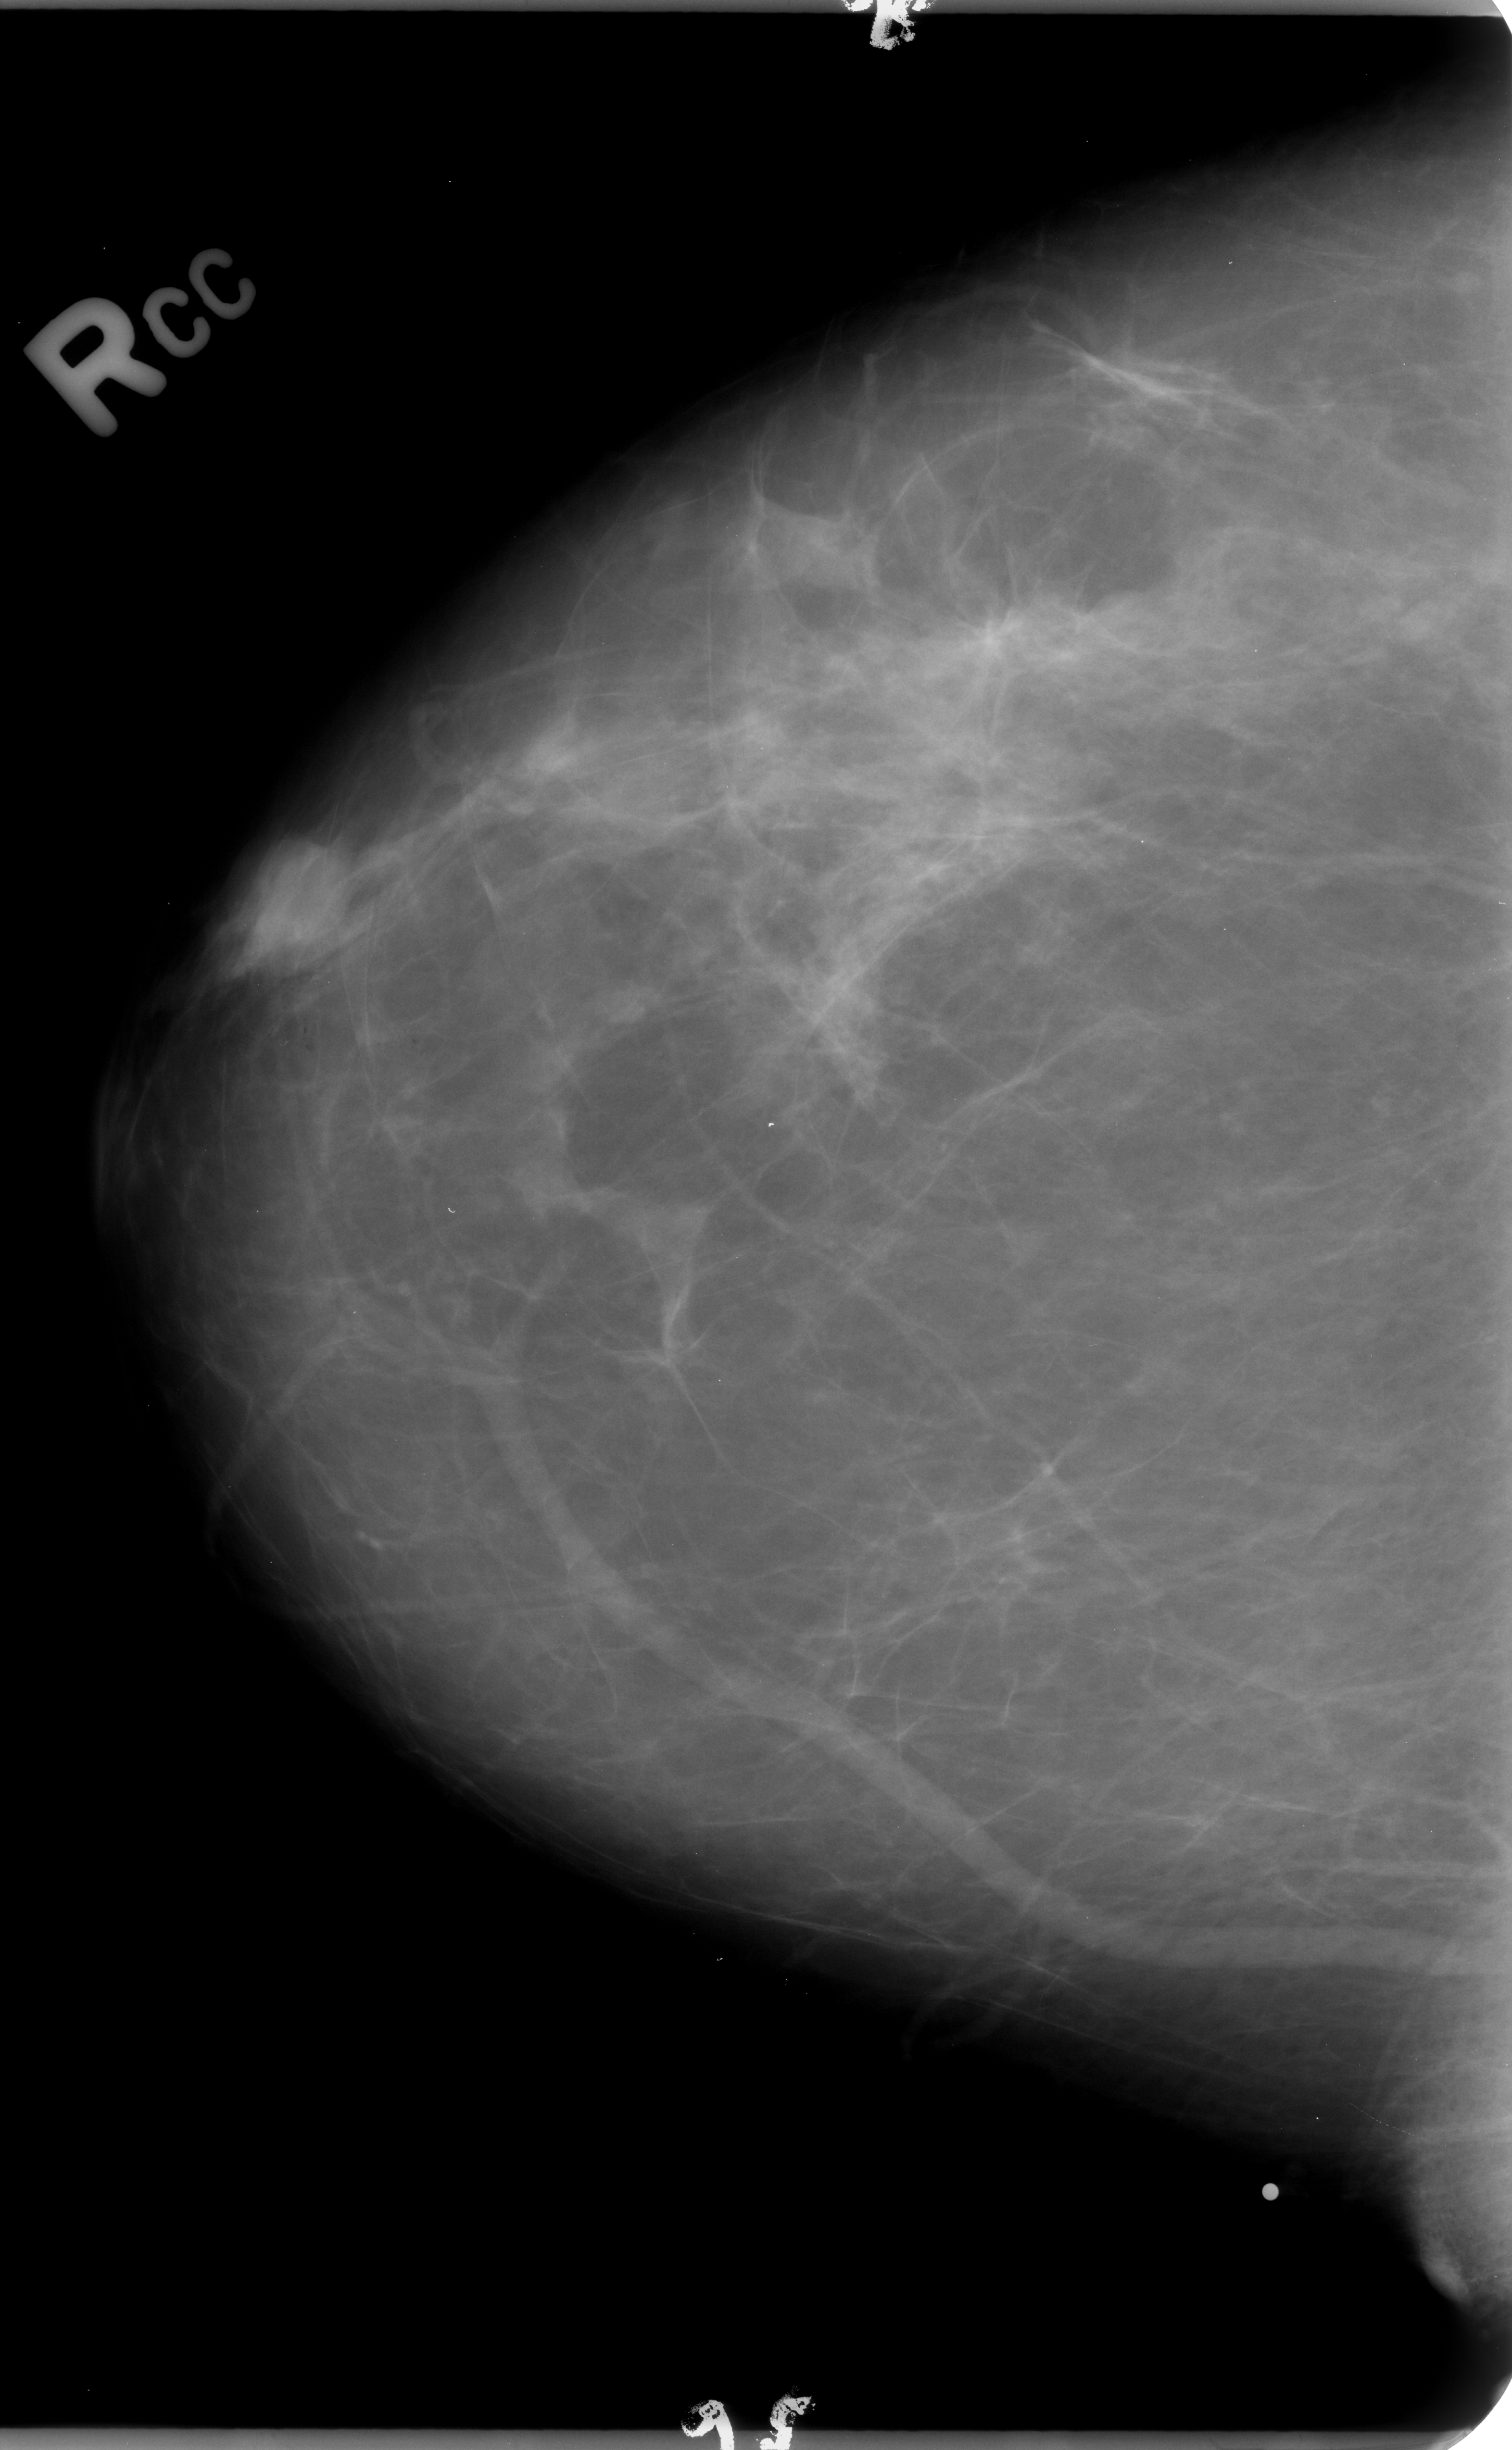
Mammogram (digitized film); right breast; CC view; breast composition: scattered fibroglandular densities (BI-RADS density category 2 of 4); 1512 × 2450 image matrix.
Expert-marked regions of interest on this film, with their recorded descriptors:
- mass, shape oval, margins circumscribed / ill defined; BI-RADS assessment category 4; subtlety rating 4 on a 1 (subtle) to 5 (obvious) scale; pathology (as recorded): benign: bounding box [x1, y1, x2, y2] px = [215, 834, 335, 979]